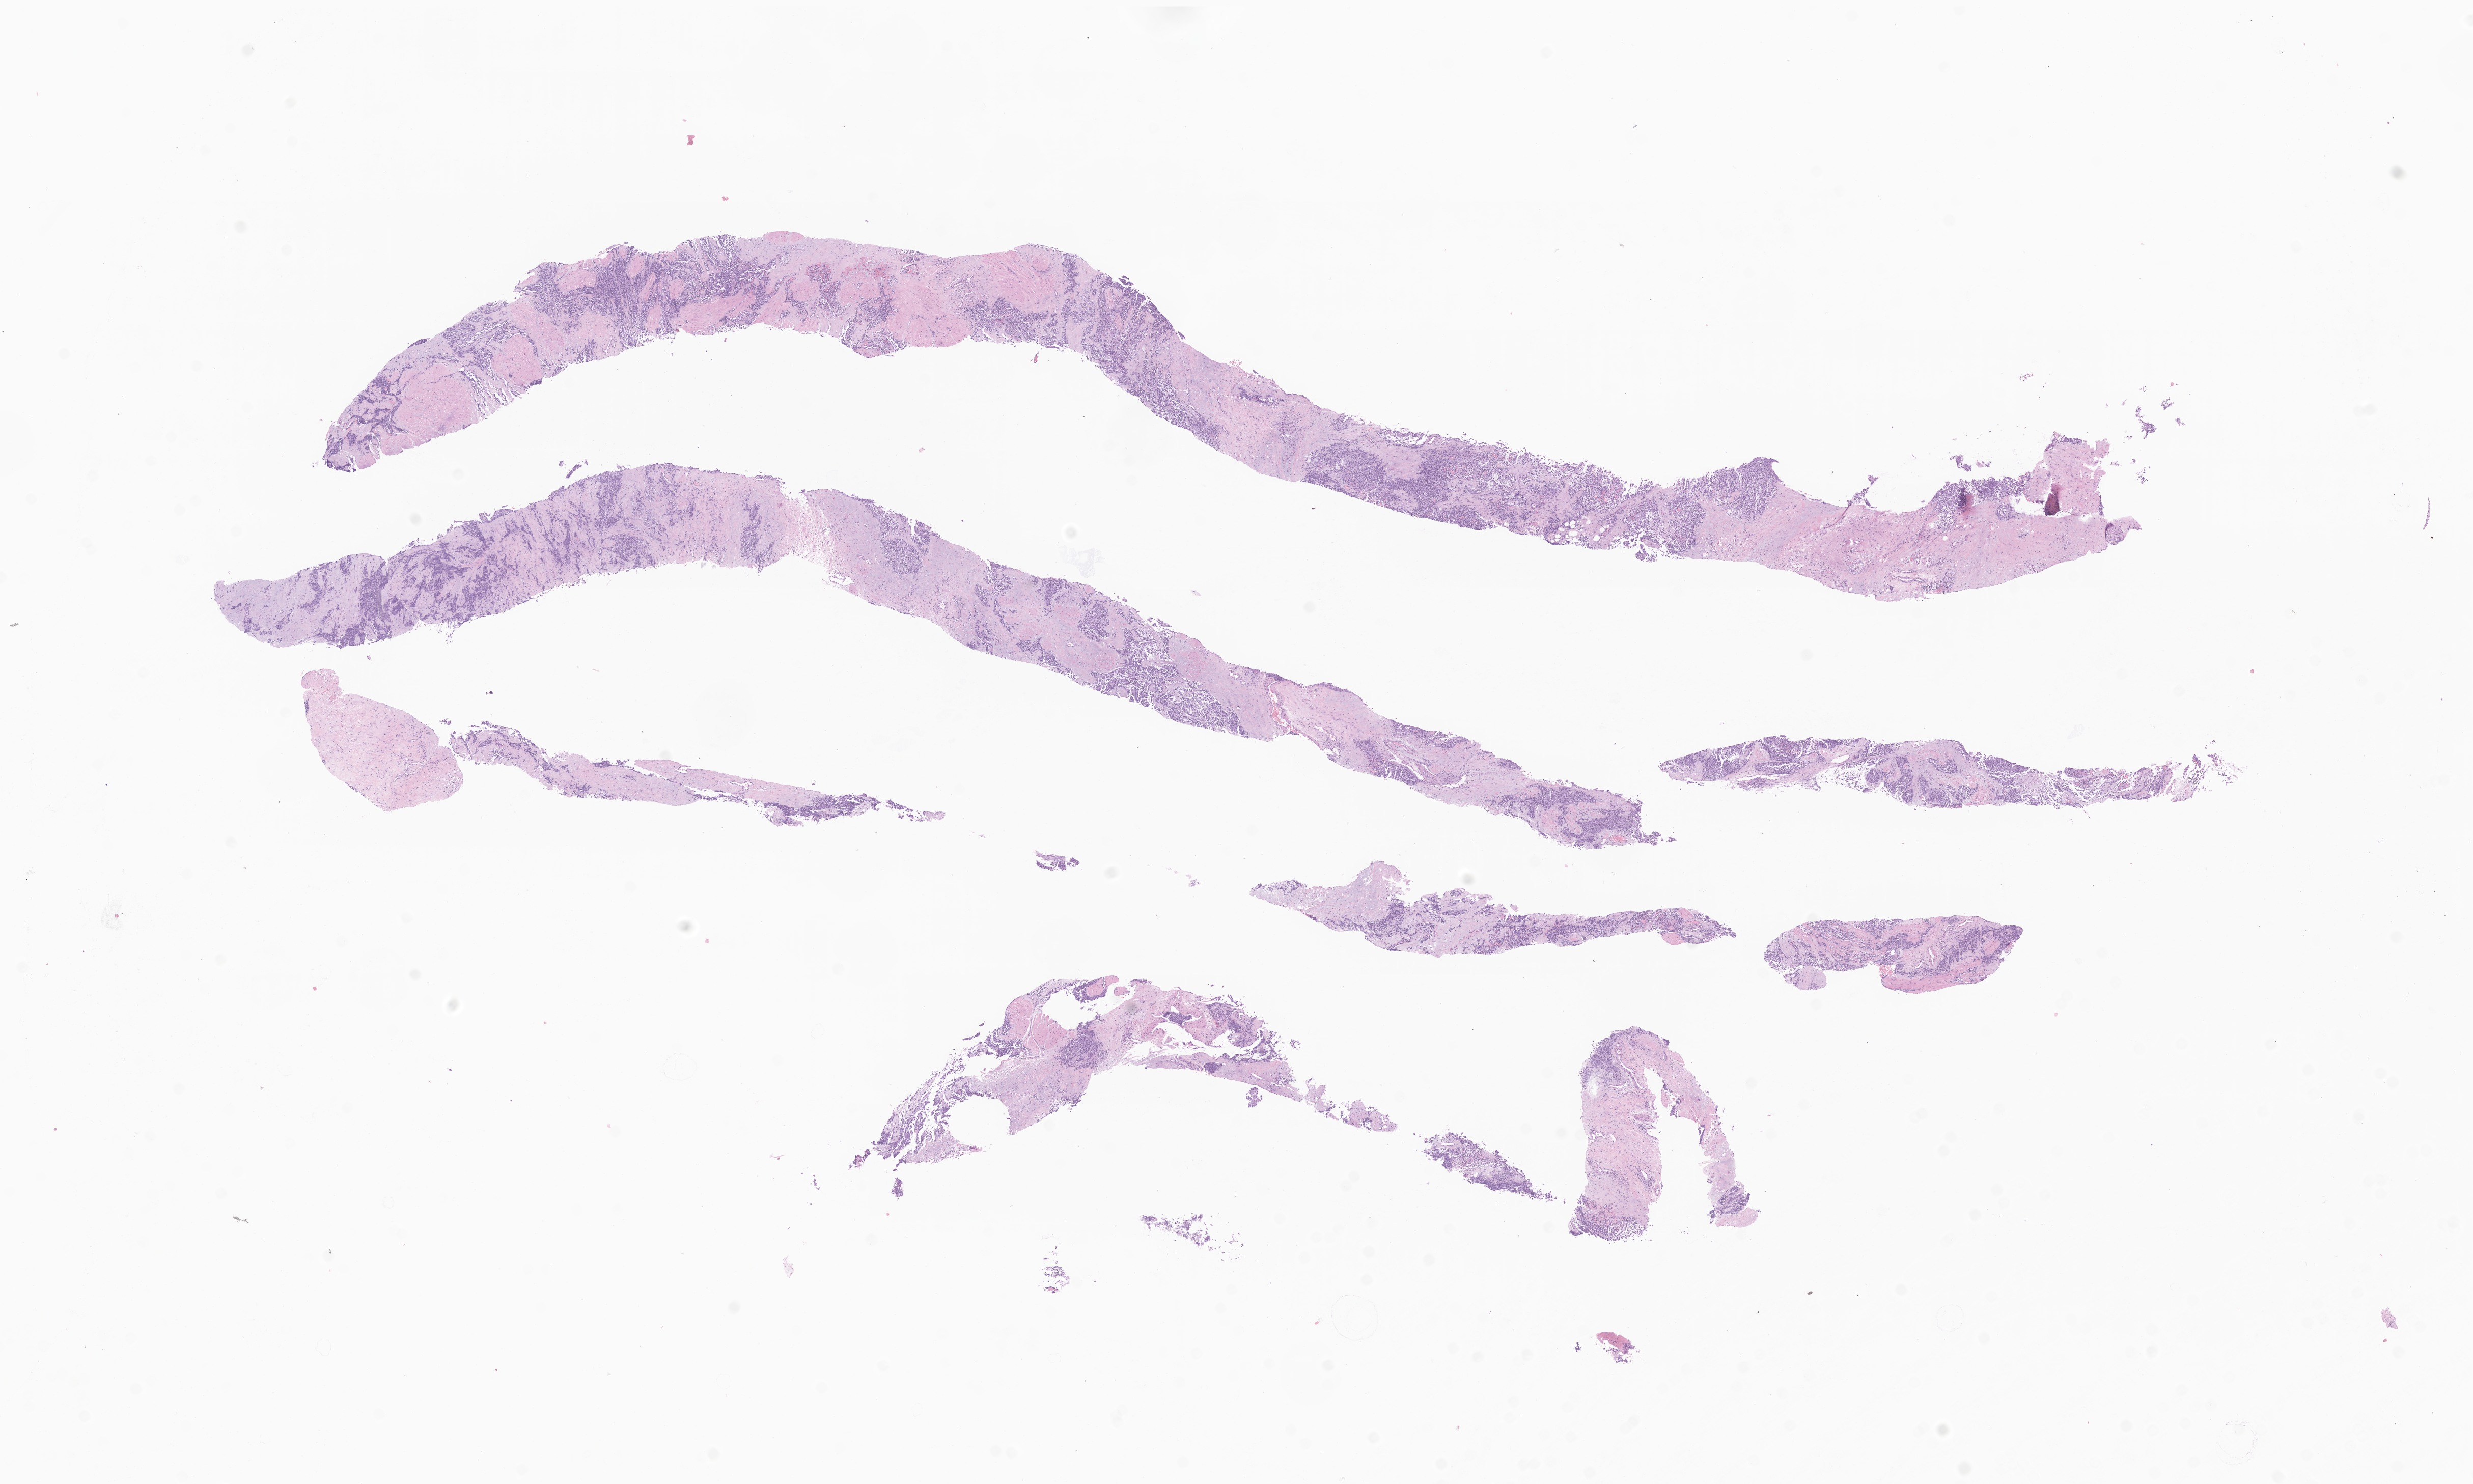
H&E whole-slide image of tumor tissue from the pelvis — whole scanned area (about 20.5 x 12.3 mm) shown as a low-resolution overview; formalin-fixed, paraffin-embedded (FFPE) tissue. Patient: male, age 204 months (17 years).
Diagnosis (ICD-O-3 morphology term): Rhabdomyosarcoma, NOS.